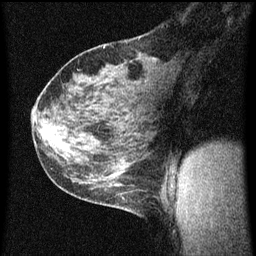
Breast MRI (dynamic contrast-enhanced), one sagittal slice; slice 34 of 60 in the series (ordered by position); dynamic contrast-enhanced series, image 2 of 3 at this slice position (ordered by acquisition); 1.5 T; TE 4.2 ms, TR 8 ms; 256 × 256 image matrix, field of view 180 × 180 mm. Female patient, age 35 years.
Structures marked on this image (semi-automatic segmentation, software-assisted and operator-edited):
- analysis volume of interest (the breast-tissue region the enhancement analysis was run in; not a lesion): bounding box (x1, y1, x2, y2) in pixels: (106, 182, 149, 217)
- tumour enhancement mask (voxels above the 70 % enhancement threshold inside the analysis volume of interest): (120, 184, 123, 187)